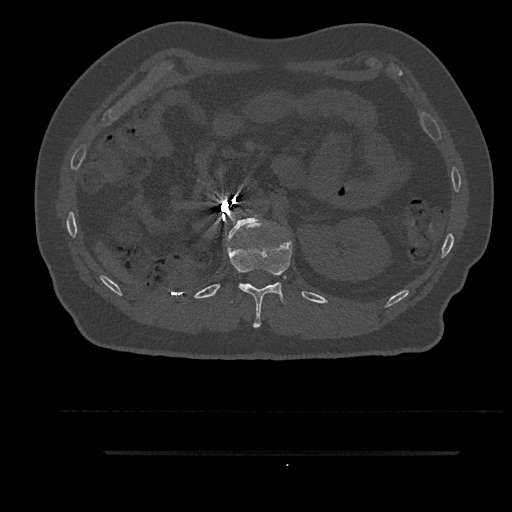
CT including the spine, one axial slice; position 226 of 797 along the scan axis; reconstruction kernel Br40s/3; bone window (W 1800 / L 400 HU); 0.5 mm slice thickness; 512 × 512 image matrix, field of view 432 × 432 mm. Male patient, age 63 years. Case-level facts recorded for this patient, not image findings: primary cancer: renal.
Outlined on this slice (semi-automatic segmentation, software-assisted and operator-edited):
- L1 vertebra: bounding box (x1, y1, x2, y2) in pixels: (226, 215, 266, 243)
- T12 vertebra: (227, 229, 292, 328)